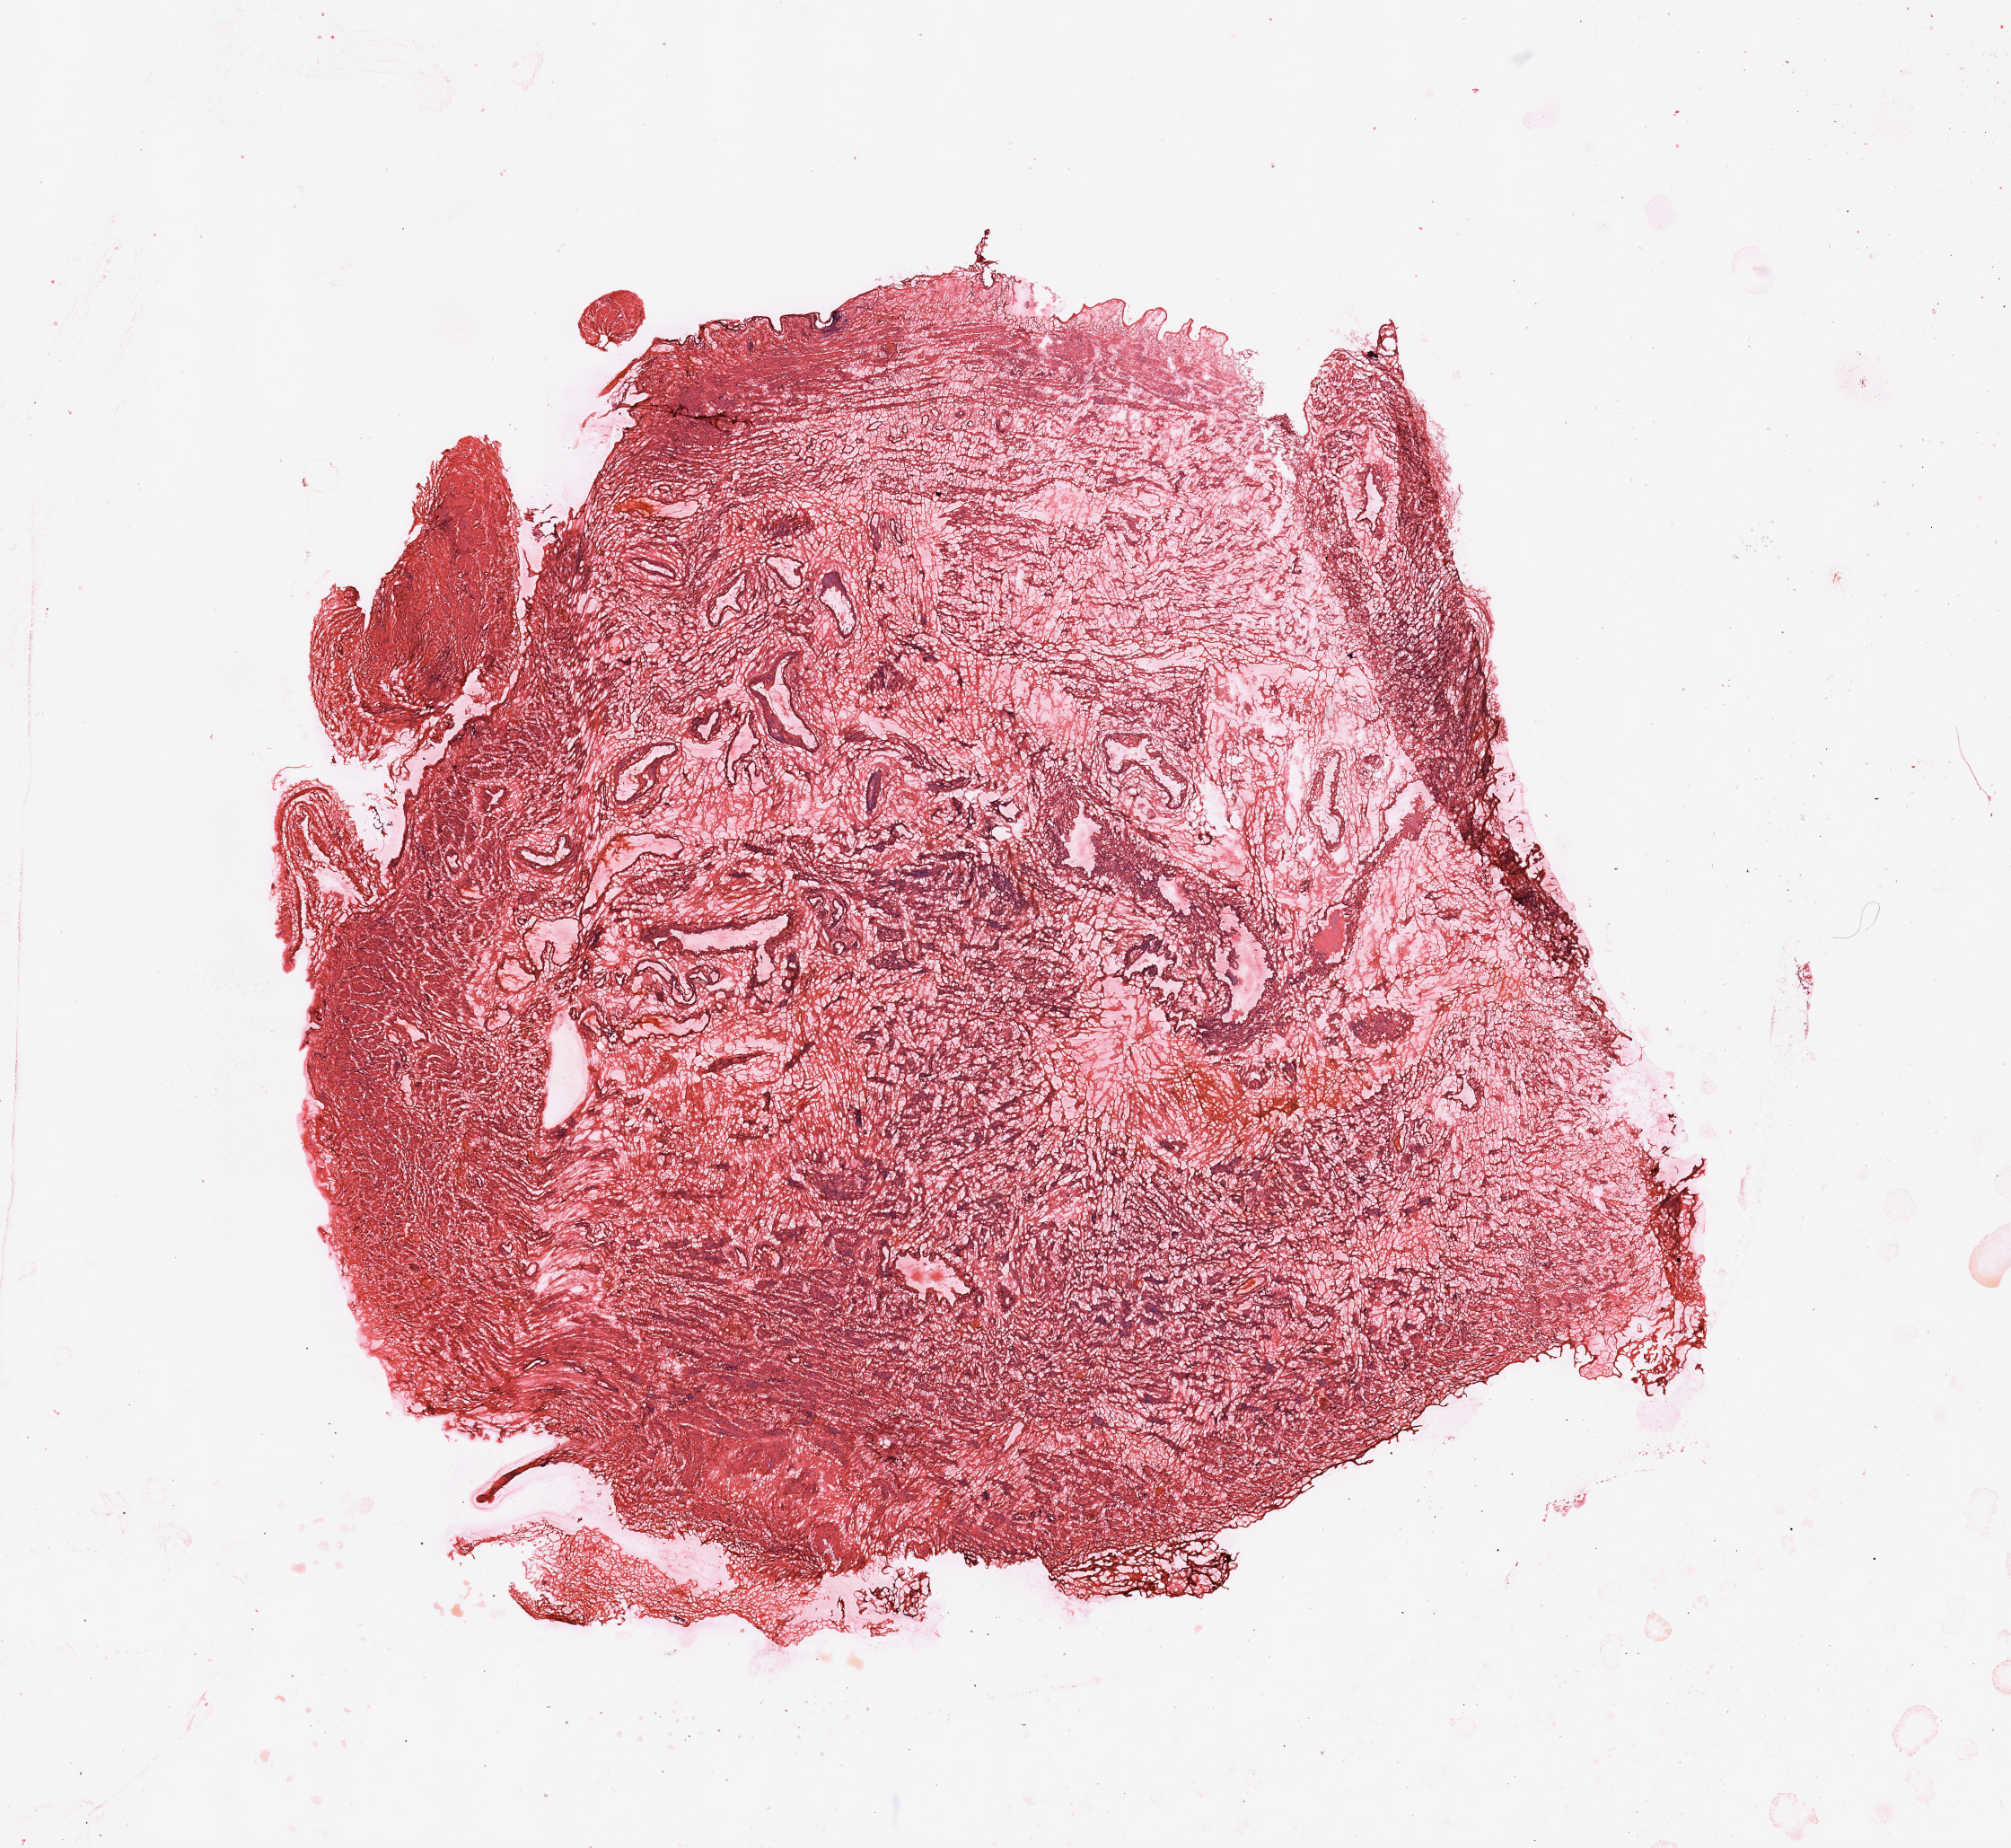
Whole-slide histology image, H&E-stained — low-resolution overview of the scanned area, about 17.7 x 16.3 mm (acquisition: 20x scan). 65-year-old female patient.
Patient diagnosis (cohort enrolment): sarcoma (site not recorded at cohort level). Primary tumour site (as recorded): gynecologic.